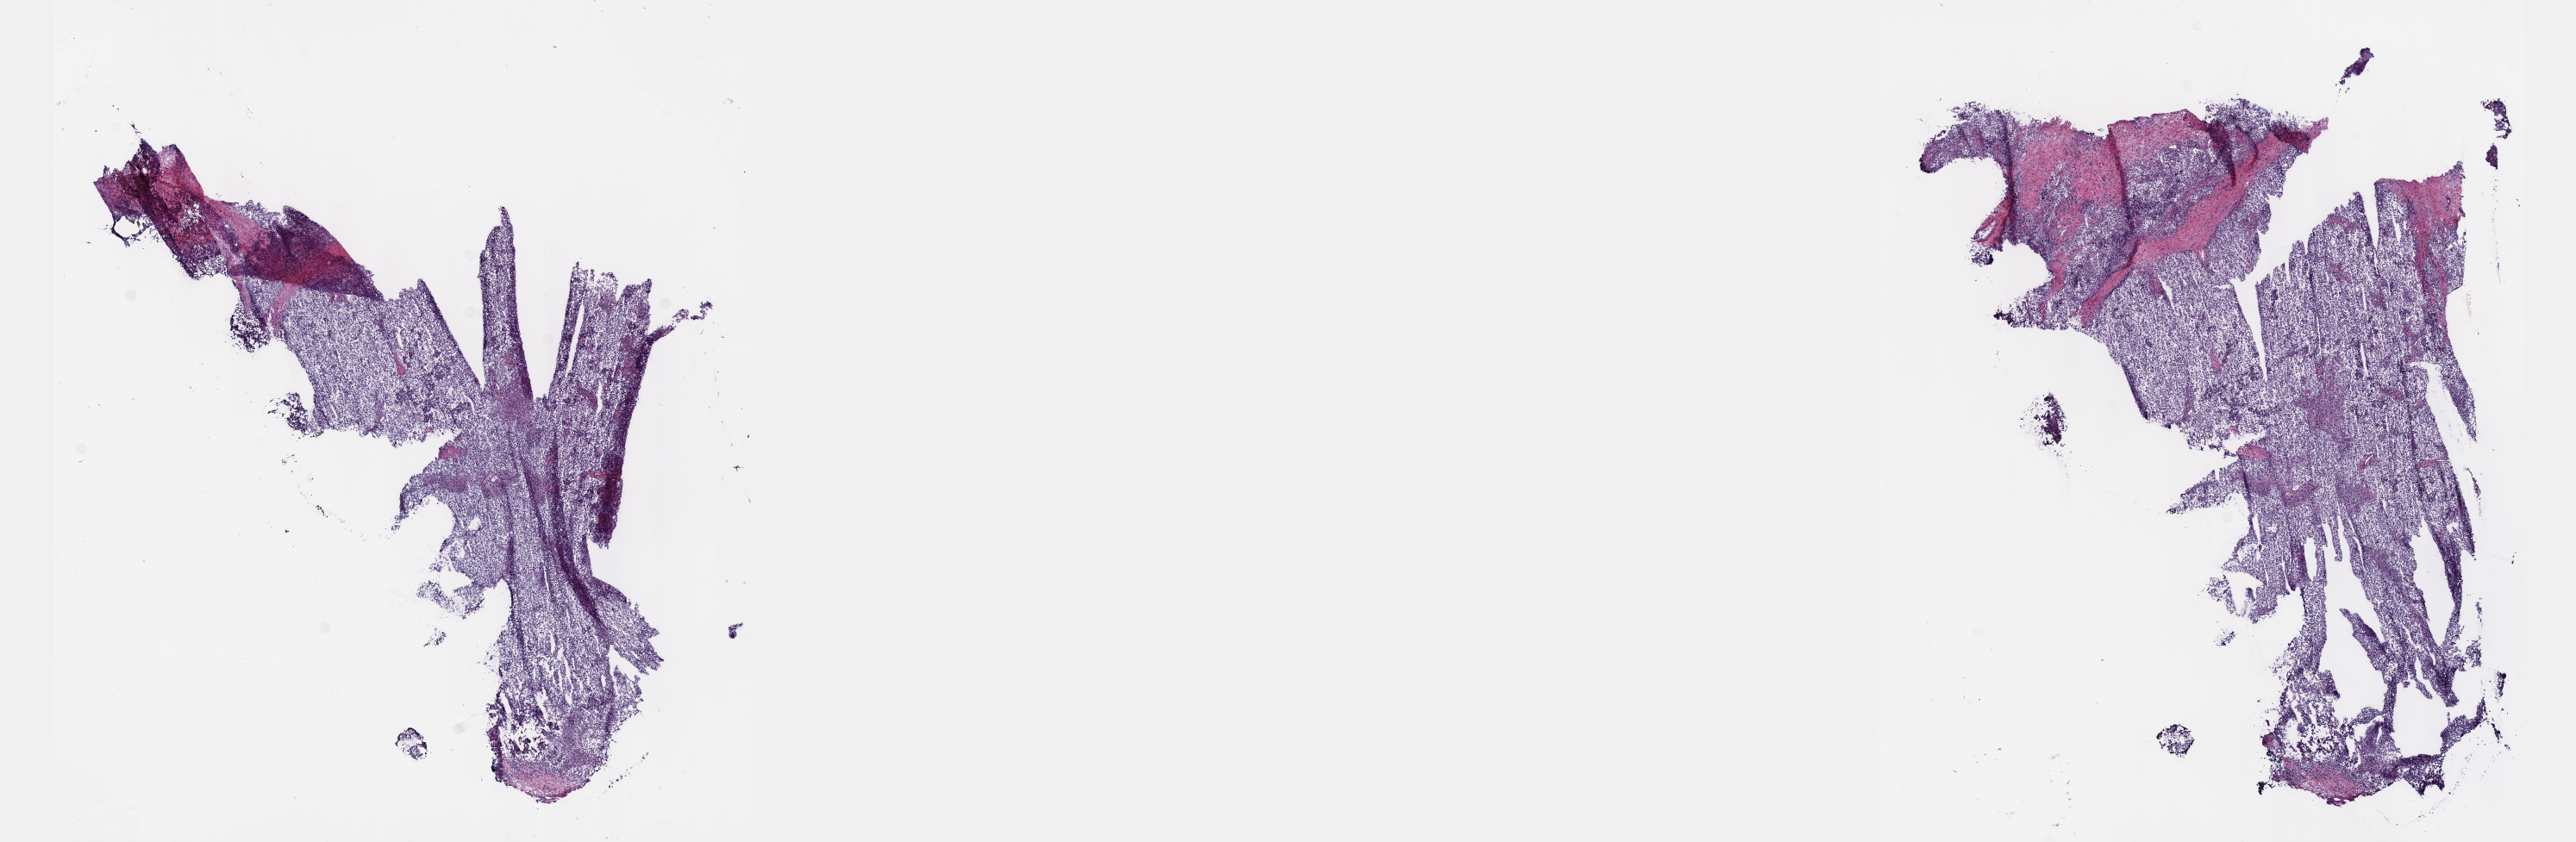
Hematoxylin and eosin (H&E) stained whole-slide image, shown as a low-resolution overview of the whole scanned area (about 24.1 x 7.9 mm), frozen section from the top of the tissue portion, testis, primary tumour sample. Male patient; age at initial diagnosis 38 years.
Histologic diagnosis: Seminoma, NOS.